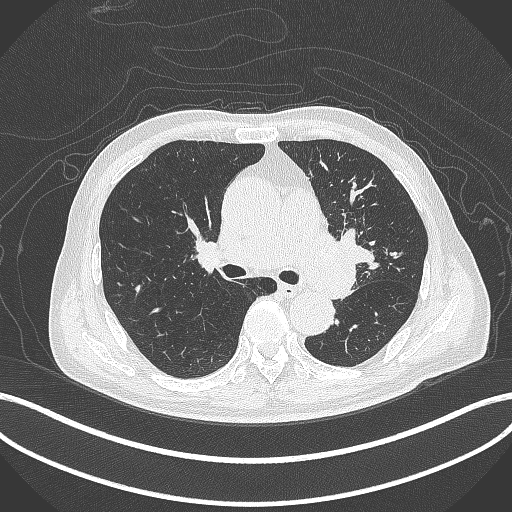
Chest CT, one axial slice. Slice 262 of 417 in the series (ordered by position). Lung window (W 1500 / L -600 HU). 512 × 512 image matrix, field of view 400 × 400 mm. Male patient, age 77 years. Case-level facts recorded for this patient, not image findings: clinical TNM (as recorded): T3 N1 M0.
Annotated regions visible in this slice (rectangle marked by the reading radiologist):
- lung tumour (recorded histology: adenocarcinoma): bounding box [x1, y1, x2, y2] px = [310, 227, 371, 301]